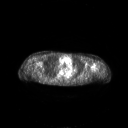
FDG PET of an extremity soft-tissue mass (from a PET/CT study), one axial slice; slice 188 of 267 in the series (ordered by position); 128 × 128 image matrix, field of view 700 × 700 mm. Patient: female, 83 years. From the clinical record (not read from this slice): histological type: pleiomorphic leiomyosarcoma; grade: high; site of the primary tumour: left biceps.
Outlined on this slice (expert contour drawn on MRI and transferred to this co-registered scan by the dataset authors):
- gross tumour volume including surrounding oedema: bounding box [x1, y1, x2, y2] px = [92, 65, 96, 70]